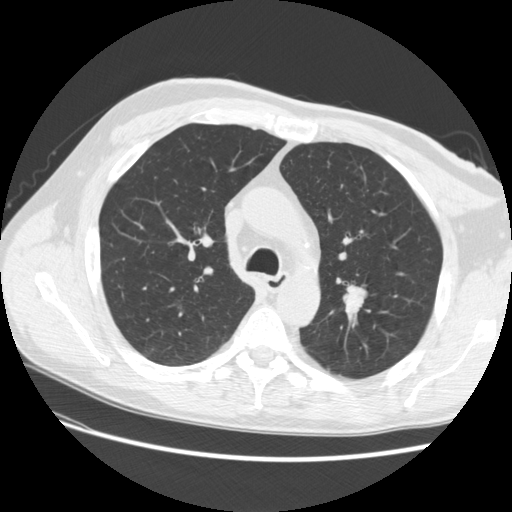
Low-dose screening chest CT, one axial slice; slice 180 of 256 in the series (ordered by position); reconstruction kernel STANDARD; lung window (W 1500 / L -600 HU); 2.5 mm slice thickness; 512 × 512 image matrix, field of view 366 × 366 mm.
Annotated regions visible in this slice (outlined manually by an expert reader):
- lesion 1 (tumor, upper lobe of left lung): bounding box (x1, y1, x2, y2) in pixels: (344, 288, 366, 314)